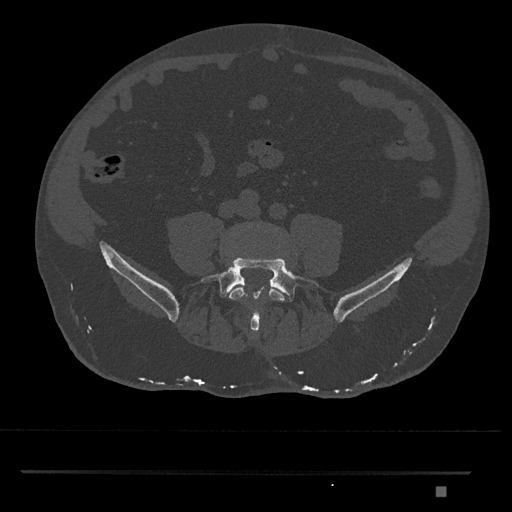
CT including the spine, one axial slice. Slice 576 of 1134 in the series (ordered by position). Reconstruction kernel Br40s/3. Bone window (W 1800 / L 400 HU). 512 × 512 image matrix, field of view 429 × 429 mm. Male patient, age 65 years. From the clinical record (not read from this slice): primary cancer: prostate.
Outlined on this slice (semi-automatic segmentation, software-assisted and operator-edited):
- L4 vertebra: box from (x=228, y=222) to (x=285, y=302) px
- L5 vertebra: (x=201, y=256)–(x=322, y=333)